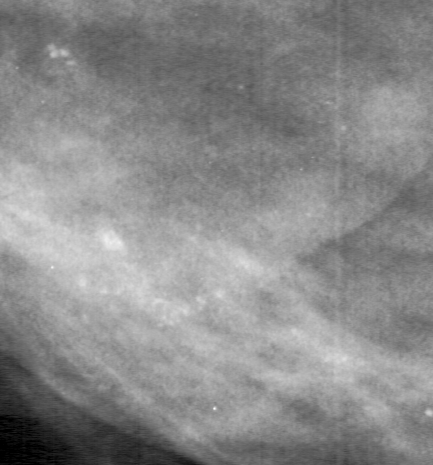
Cropped region of a digitized screen-film mammogram centred on a radiologist-marked abnormality; right breast; MLO view; BI-RADS breast density category 4 (scale 1–4).
Finding: calcifications, morphology pleomorphic, distribution clustered; BI-RADS assessment category 4; pathology result (as recorded, not read from the image): benign.